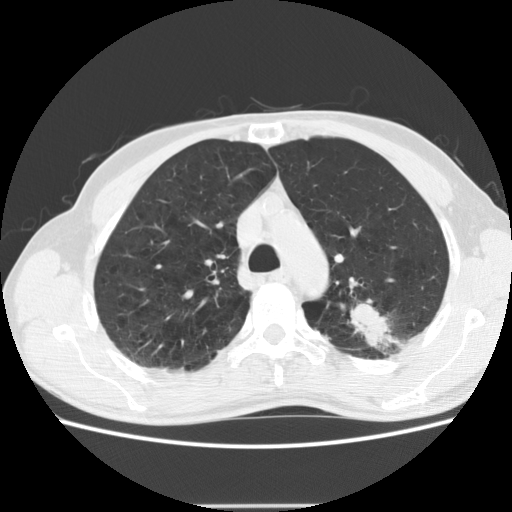
Low-dose screening chest CT, axial slice. Baseline annual screen. Lung window (W 1500 / L -600 HU). 2.5 mm slice thickness. 120 kVp. 512 × 512 image matrix, field of view 352 × 352 mm. Male, age 64 years at enrolment. Current smoker at enrolment.
Expert-annotated lung lesion, bounding box <339,283,436,360> (left, top, right, bottom; pixels). Reader record for this screening exam (exam-level; its link to the box is not recorded): non-calcified nodule or mass ≥4 mm, left upper lobe, 27 × 19 mm, poorly defined margins, soft tissue attenuation. Lung cancer was diagnosed 23 days after this screen: adenocarcinoma, NOS, left upper lobe, moderately differentiated (G2), stage IA (AJCC 6th edition), 29 mm at pathology.